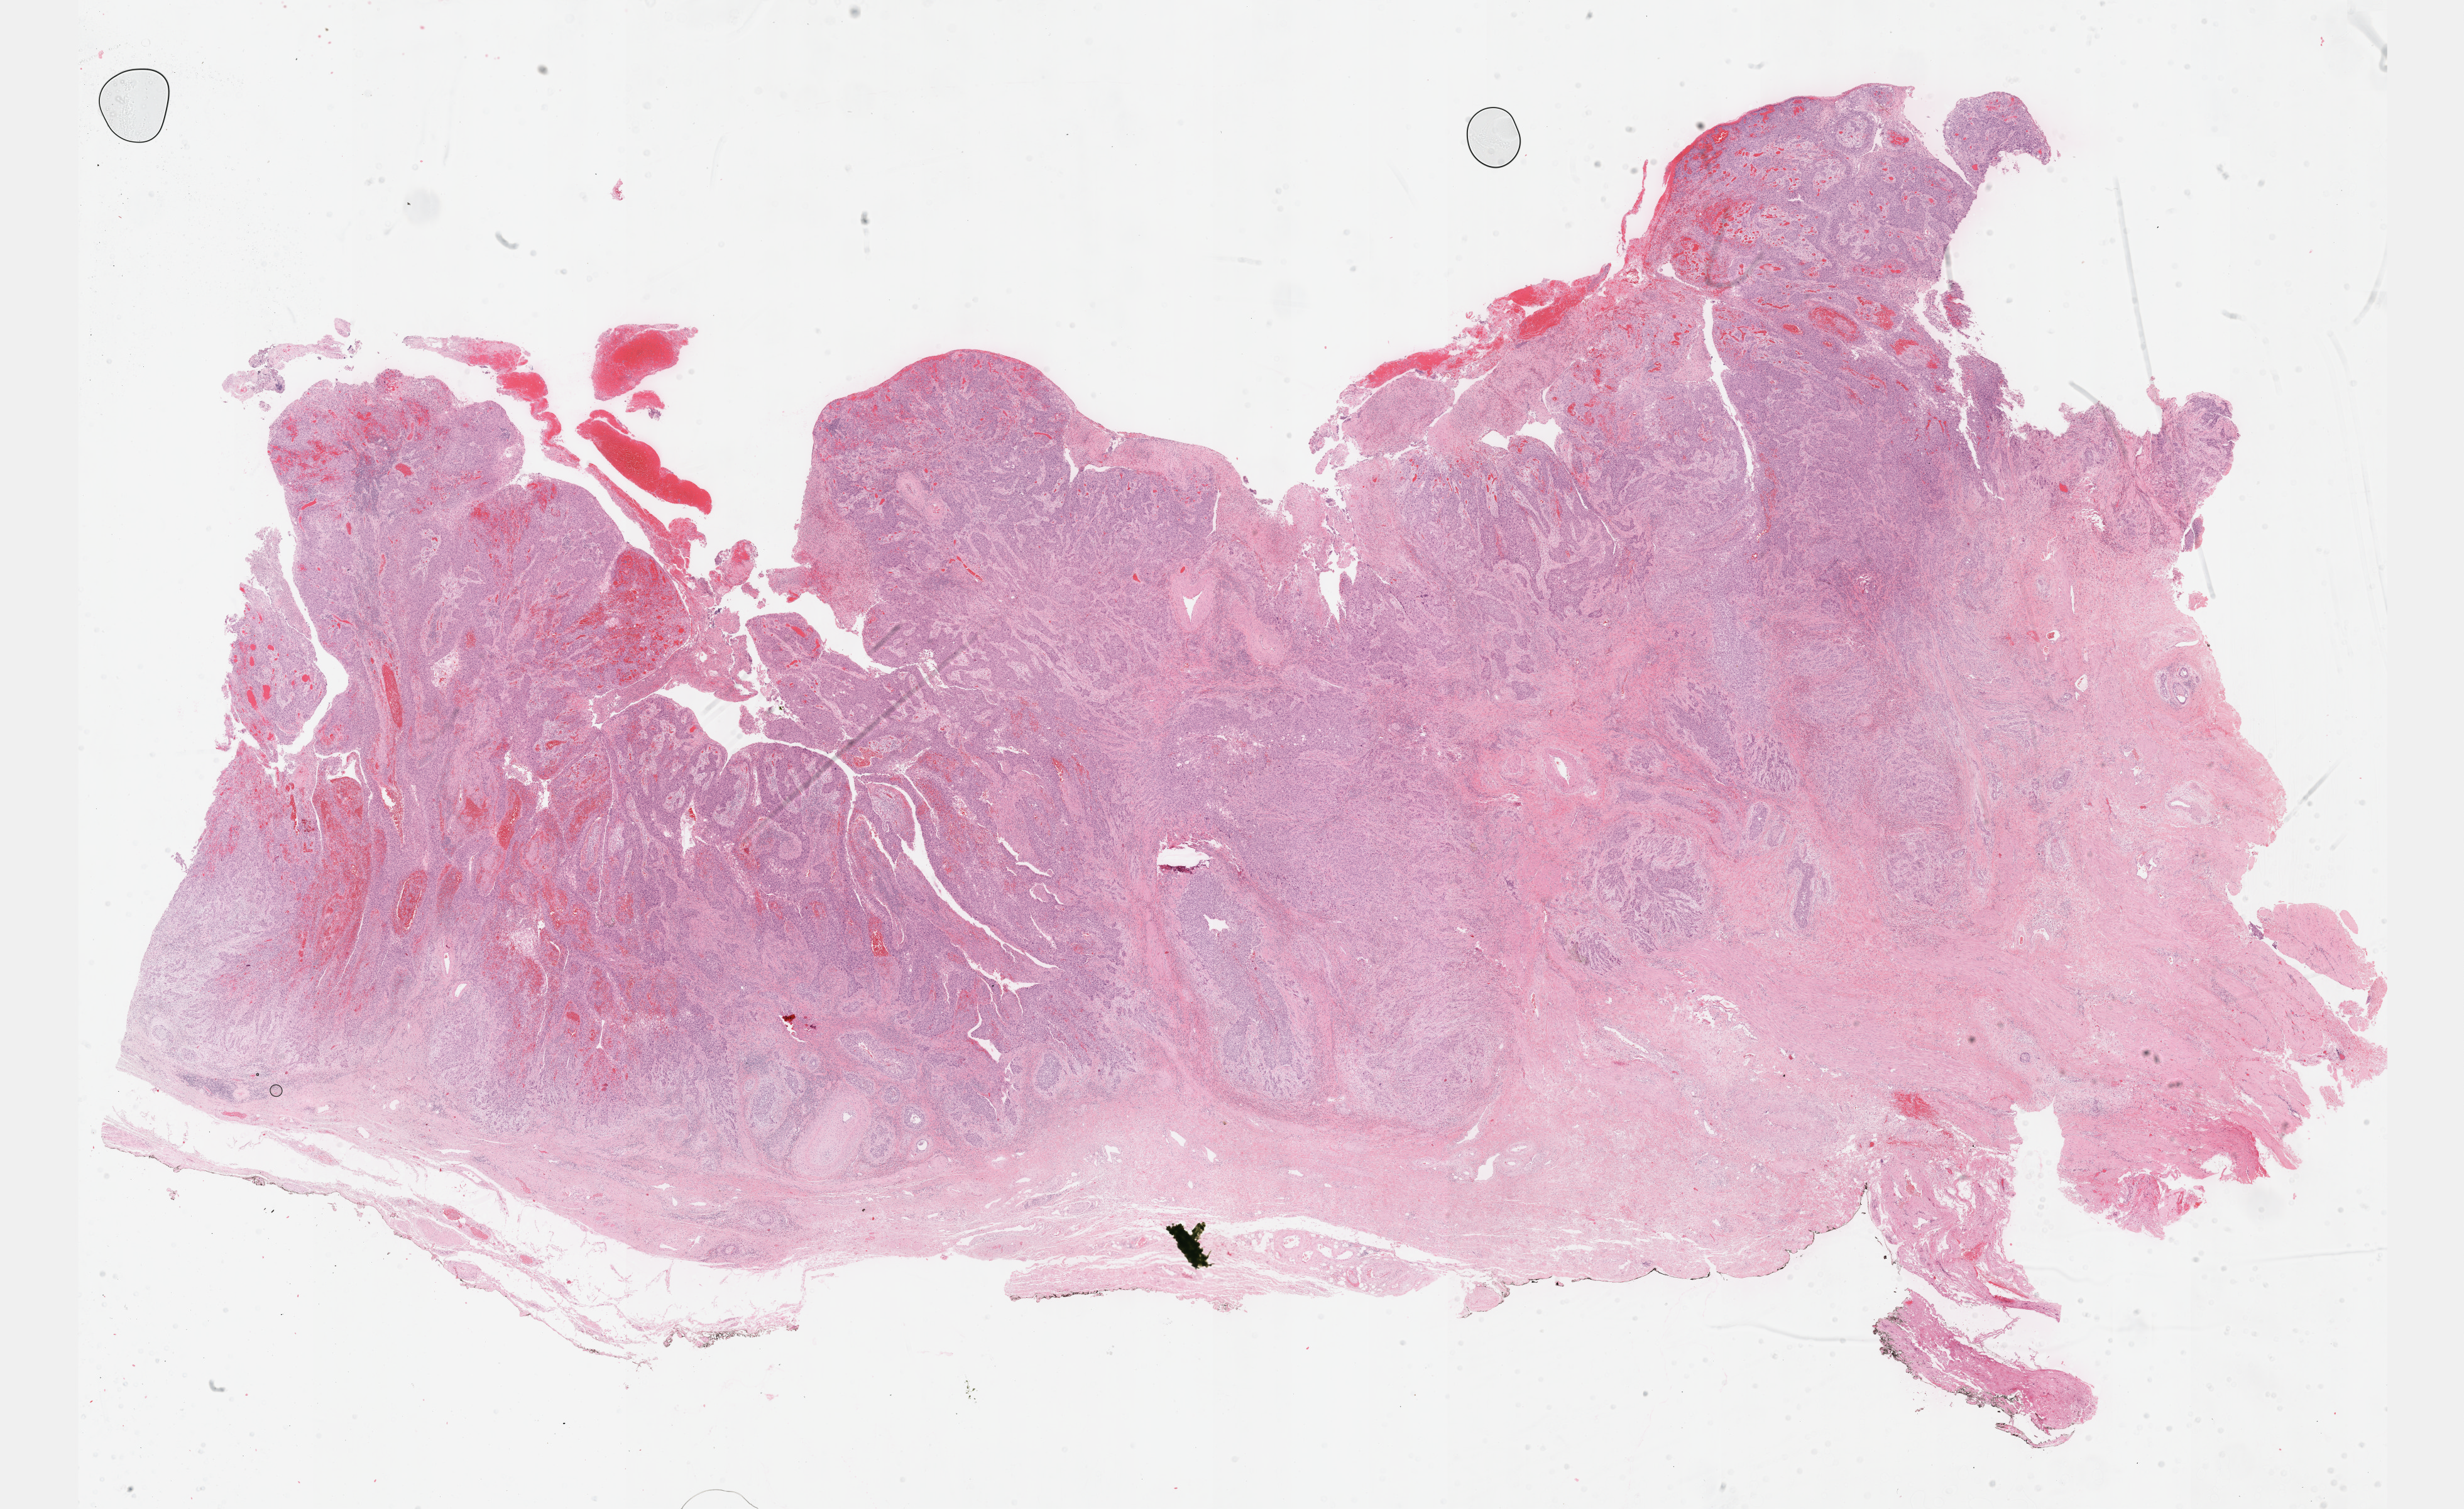
H&E whole-slide image, a low-resolution overview of the entire scanned area, about 31.7 x 19.4 mm (slide scanned at 40x); formalin-fixed paraffin-embedded (FFPE) diagnostic section; primary tumour sample from the cervix. Female patient; age at initial diagnosis 21 years. Histologic grade: G2 (moderately differentiated).
- diagnosis: Squamous cell carcinoma, keratinizing, NOS (cervix uteri)
- FIGO stage: IB
- lymph nodes positive (case pathology): 0 of 11 examined